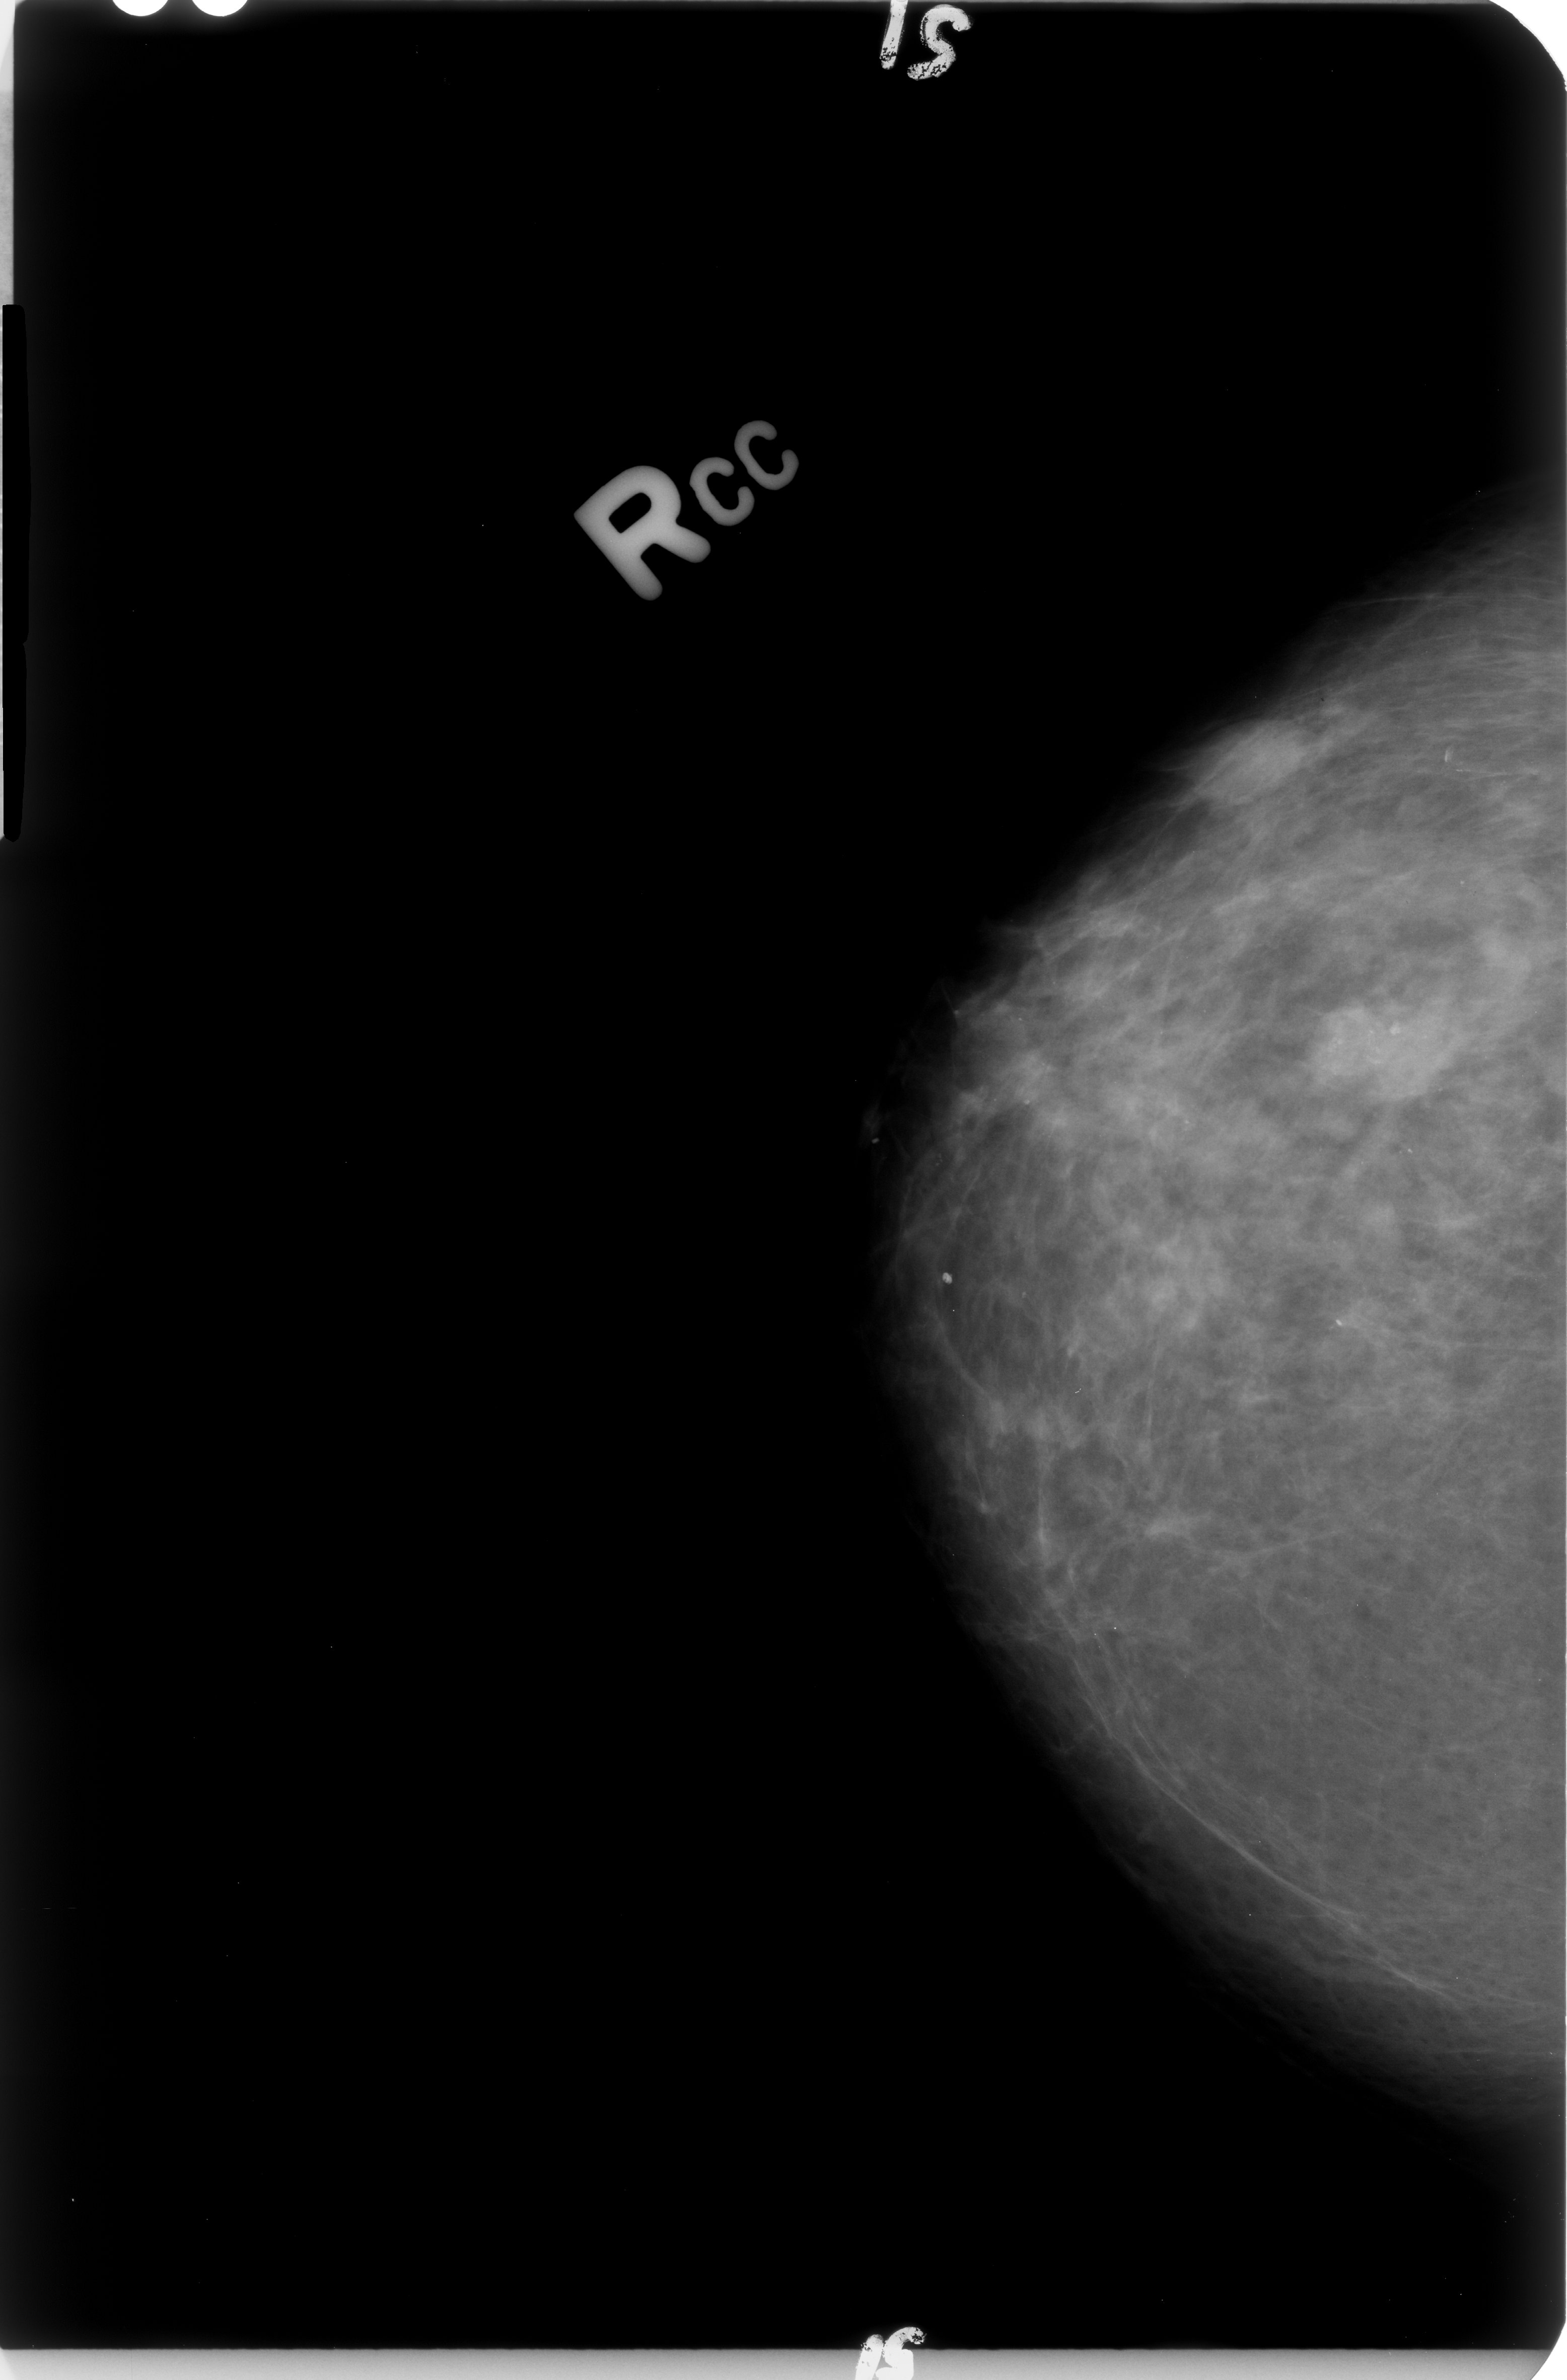
Scanned film-screen mammogram; right breast; CC view; BI-RADS breast density category 2 (scale 1–4).
Finding: calcifications, morphology pleomorphic, distribution clustered; BI-RADS assessment category 4; subtlety rating 3 on a 1 (subtle) to 5 (obvious) scale; pathology result (as recorded, not read from the image): malignant.